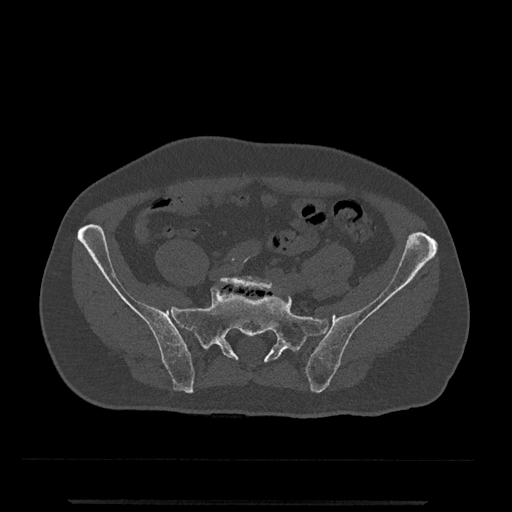
CT including the spine, one axial slice; position 17 of 797 along the scan axis; bone window (W 1800 / L 400 HU); 512 × 512 image matrix. Patient: male, 63 years. From the clinical record (not read from this slice): primary cancer: prostate.
Outlined on this slice (semi-automatically segmented with operator editing):
- L5 vertebra: bounding box (x1, y1, x2, y2) in pixels: (219, 275, 276, 291)